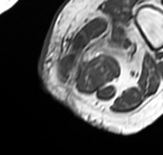
MRI of an extremity soft-tissue mass, one axial slice. Position 12 of 65 along the scan axis. MR volume resampled by the dataset authors to the PET/CT grid (not the native acquisition matrix). 163 × 155 image matrix, field of view 159 × 151 mm. Female patient. From the clinical record (not read from this slice): histological type: pleomorphic leiomyosarcoma; grade: high; site of the primary tumour: left thigh.
Outlined on this slice (expert contour drawn on MRI and transferred to this co-registered scan by the dataset authors):
- gross tumour volume including surrounding oedema: box from (x=58, y=12) to (x=143, y=84) px